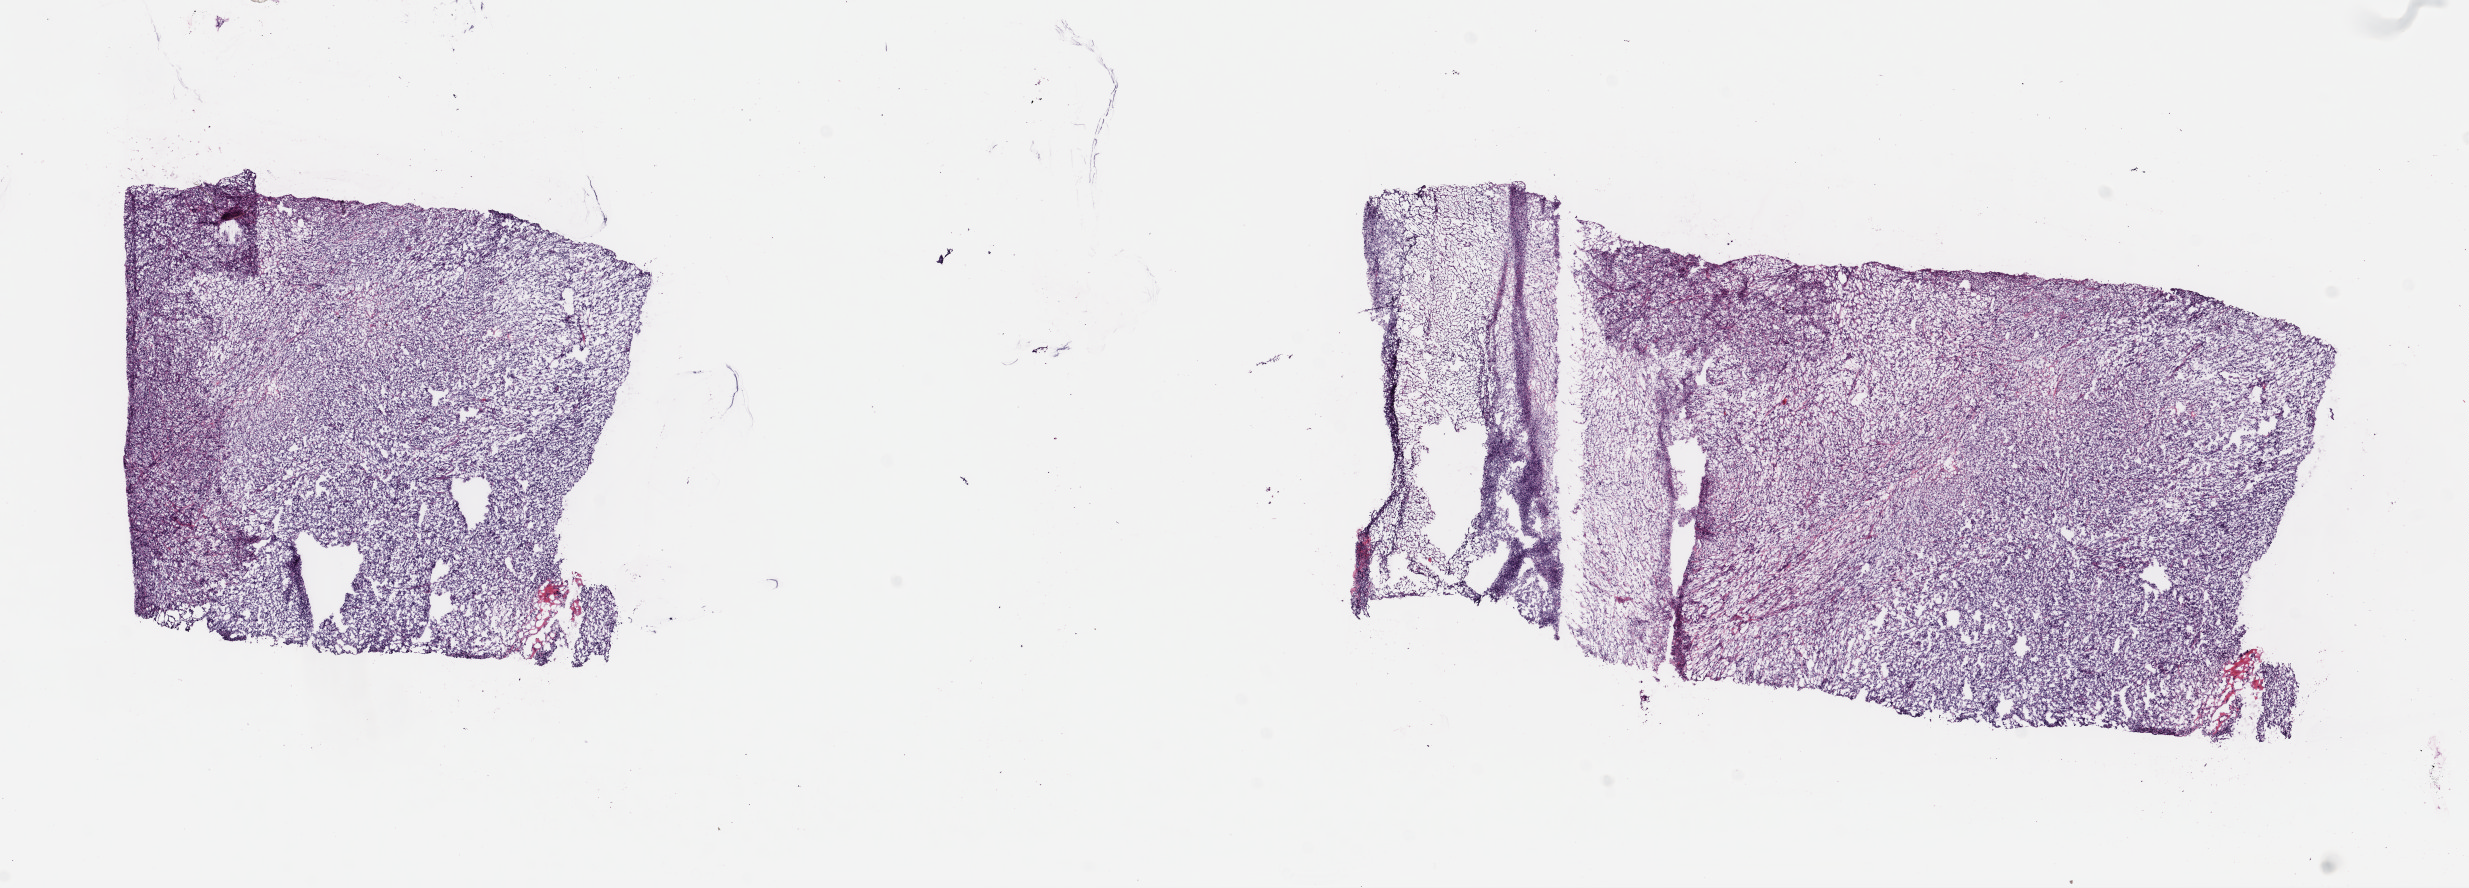
Whole-slide histology image, Hematoxylin and eosin (H&E) stained, shown as a low-resolution overview of the whole scanned area (about 19.4 x 7.0 mm, slide scanned at 40x). Frozen section. Metastatic tumour sample. Male patient; age at initial diagnosis 50 years.
This section: metastatic tumour tissue. Patient diagnosis: Malignant melanoma, NOS.